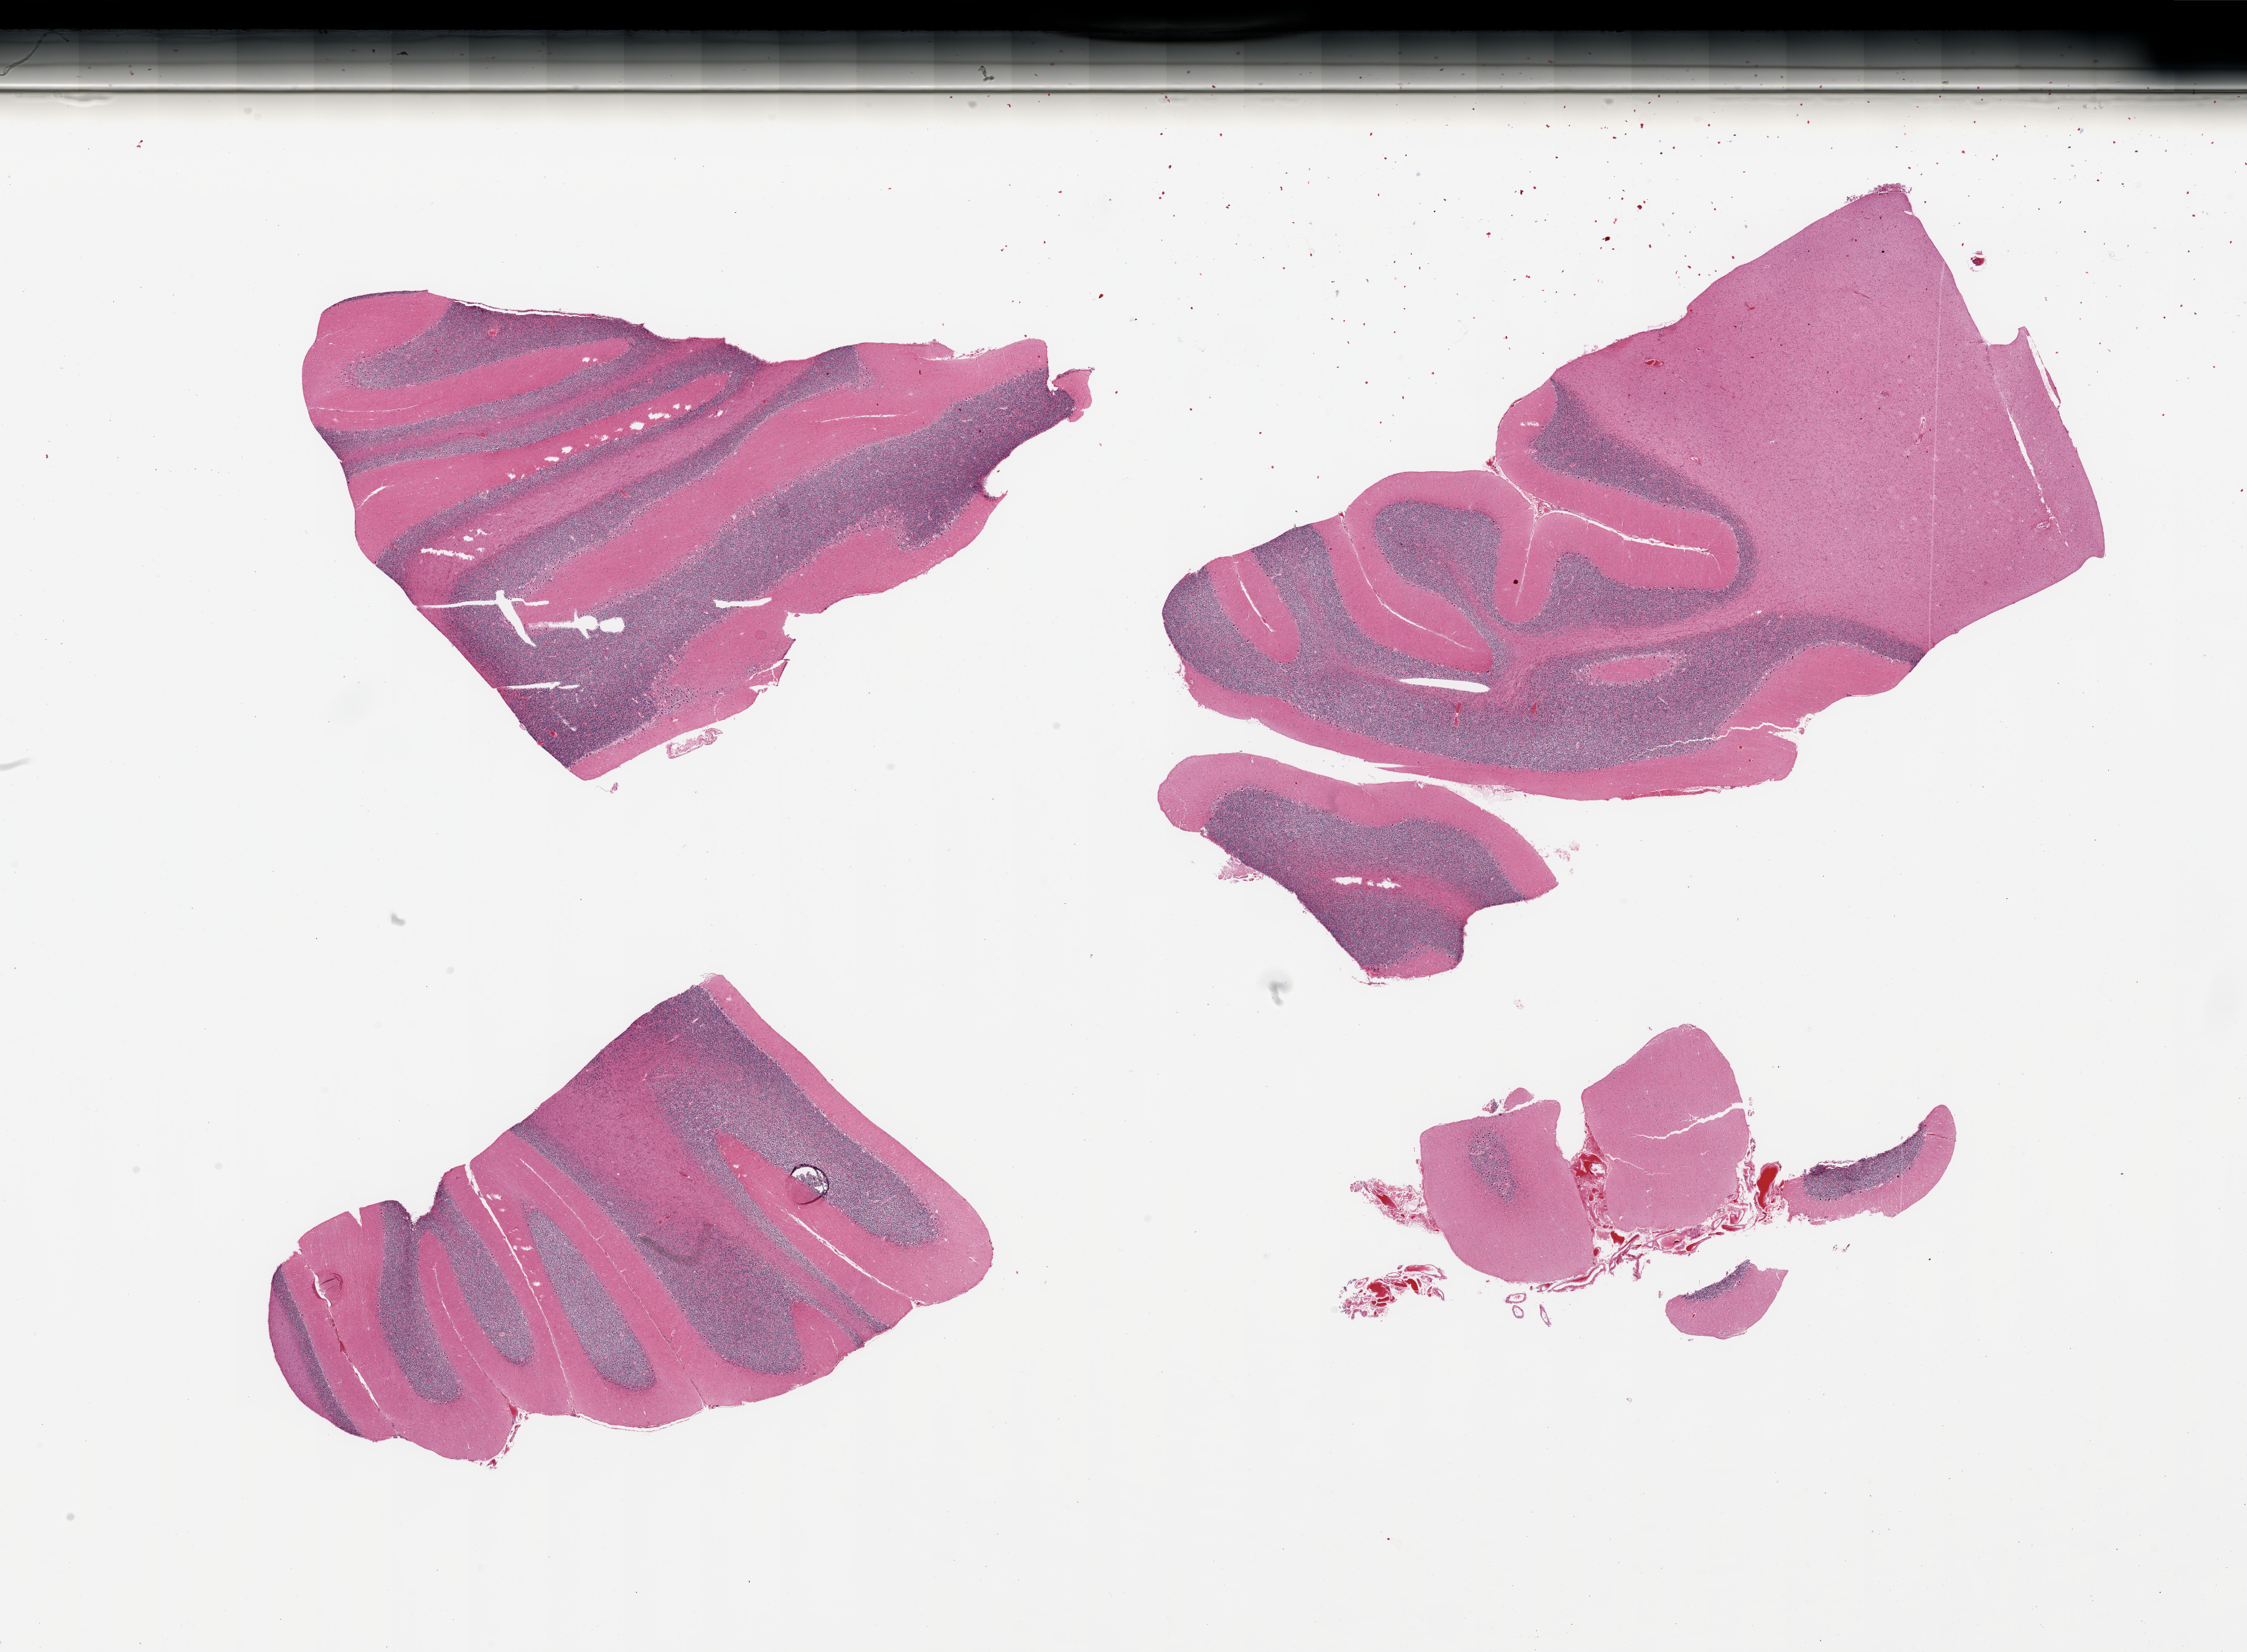
Digitized hematoxylin and eosin (H&E)-stained section — low-resolution overview of the scanned area, about 28.5 x 21.0 mm (from a 20x scan), PAXgene-fixed paraffin-embedded (PFPE) section, section of cerebellum (target tissue), donor tissue sample. Donor: male.
Review note (as recorded): 4 partially fragmented pieces.